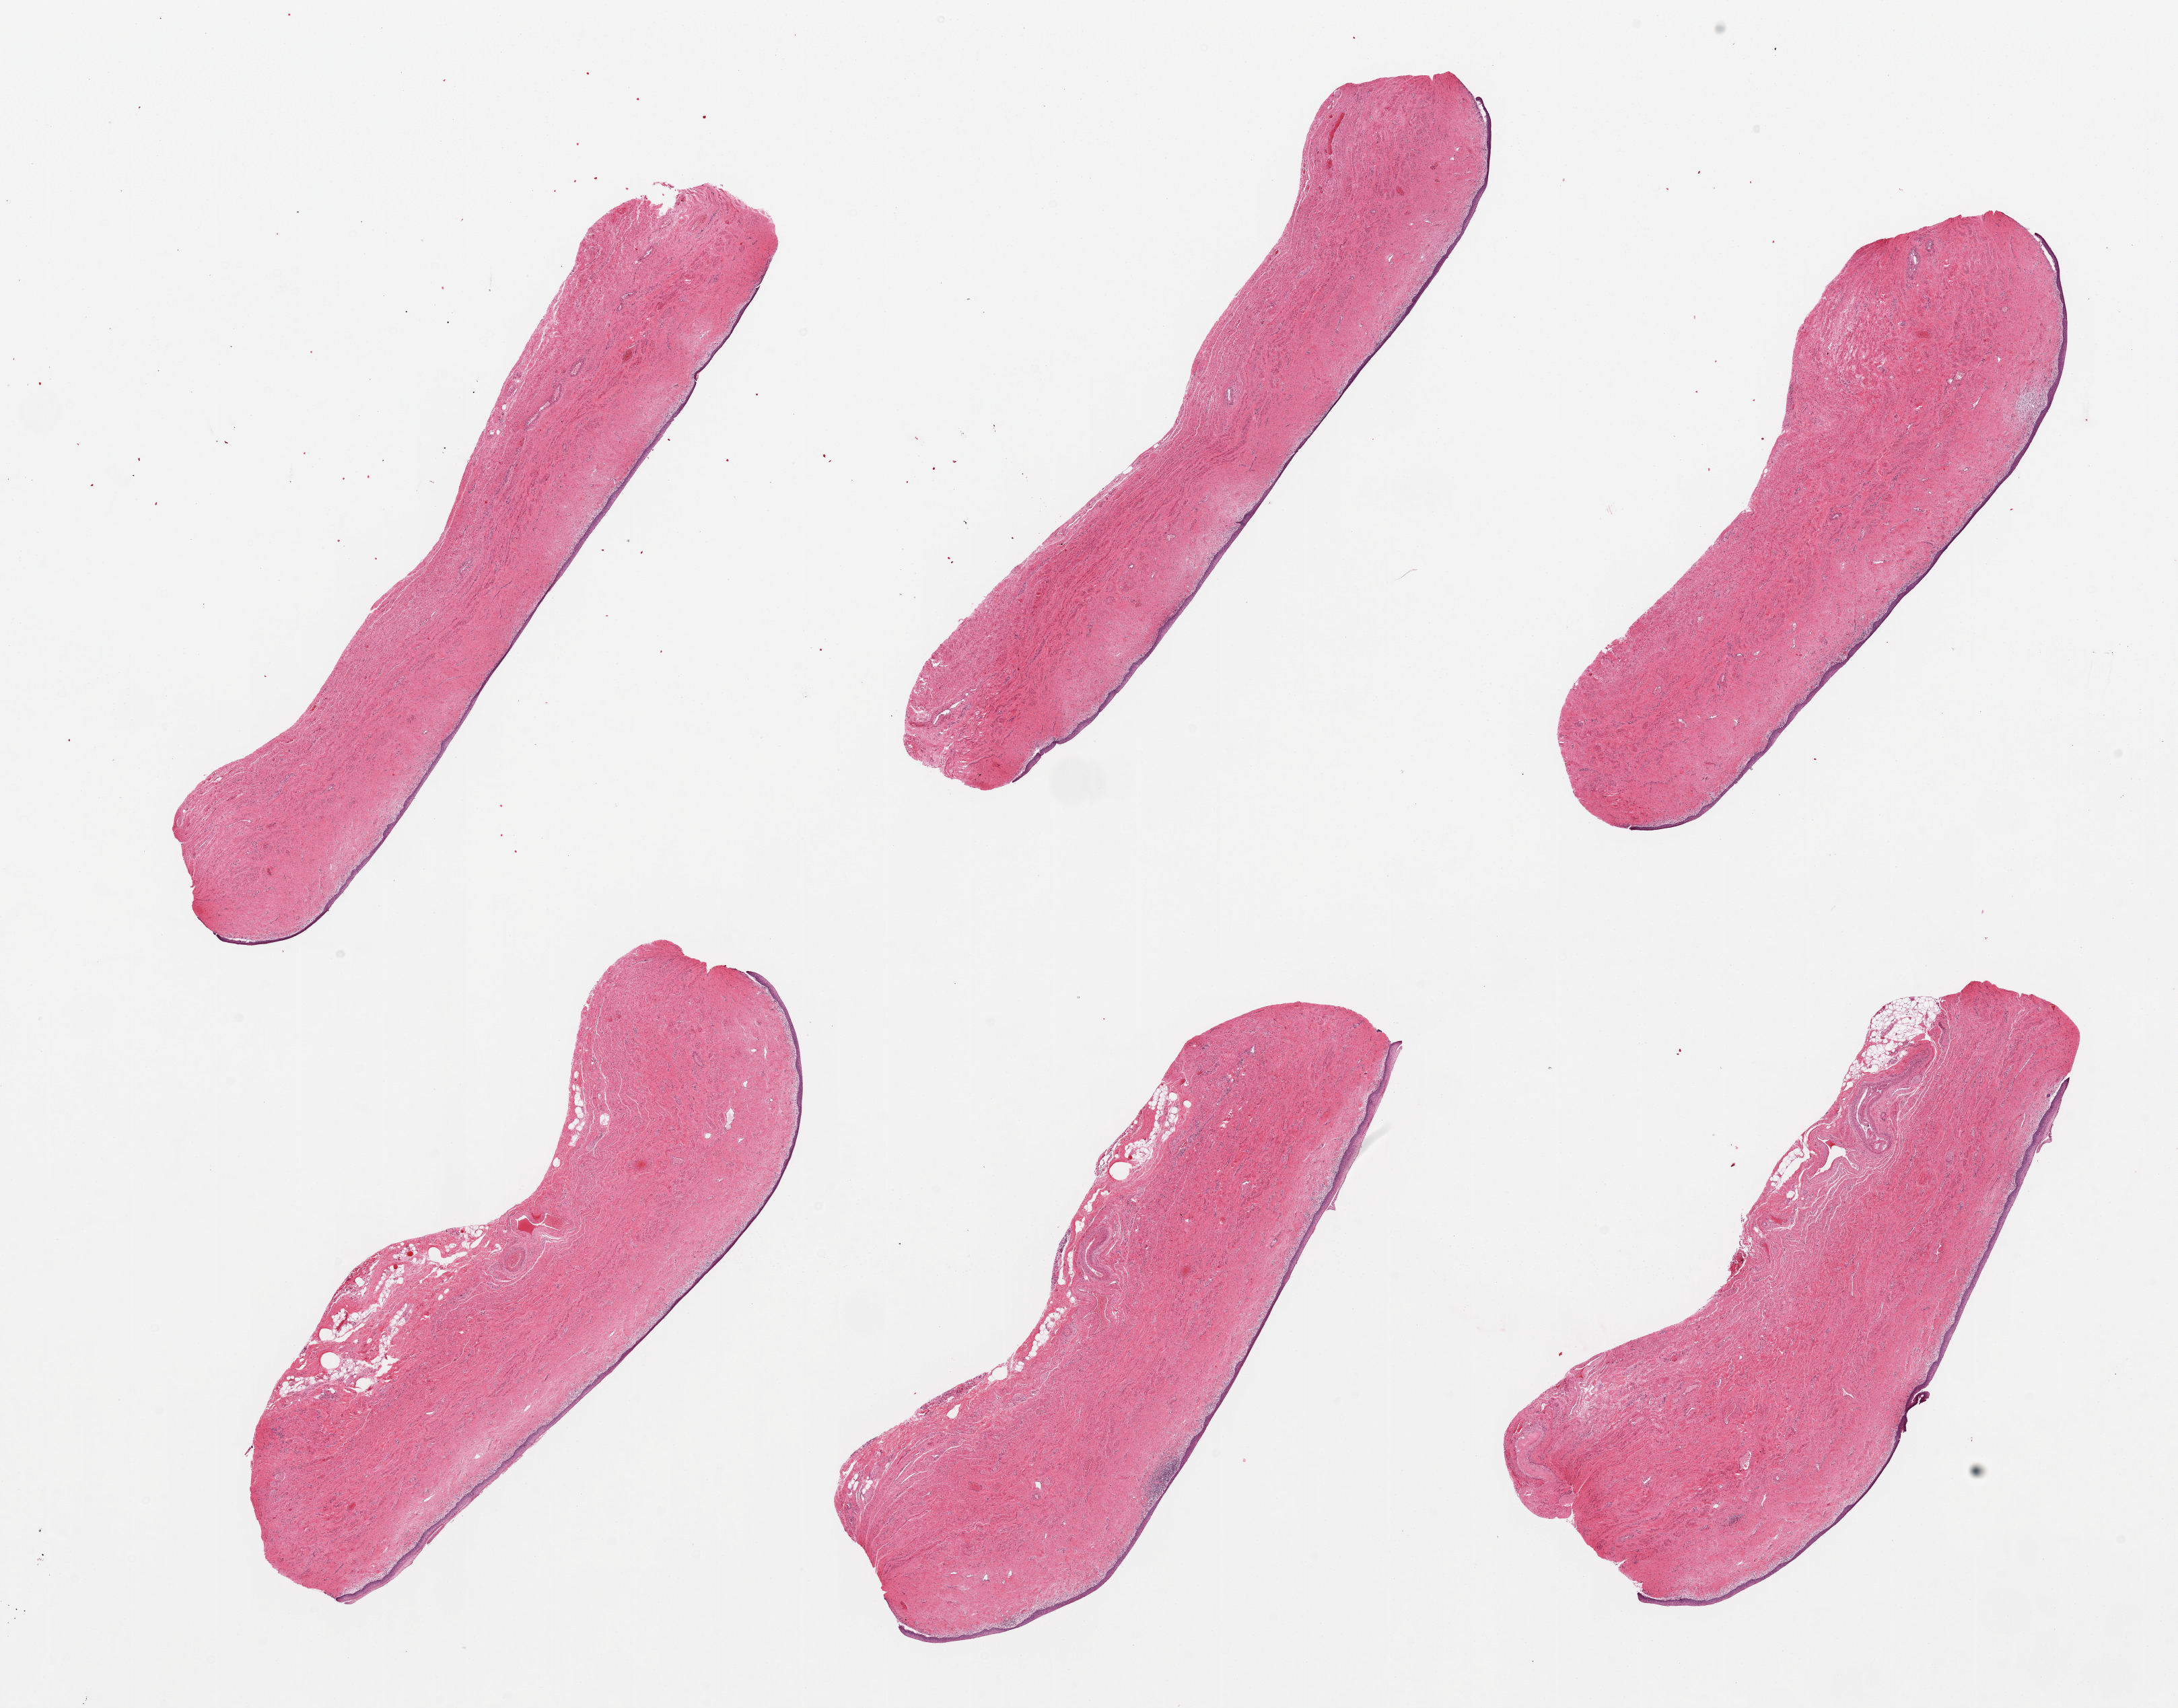
H&E whole-slide image — low-resolution overview of the scanned area, about 25.6 x 20.1 mm (from a 20x scan). PAXgene-fixed paraffin-embedded (PFPE) section. Target tissue: vagina. Donor tissue sample. Donor: female.
Reviewer comment on this tissue sample: 6 pieces, quamous mucosa ~50 microns, beginning to slough.